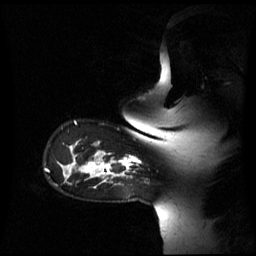
Breast MRI (dynamic contrast-enhanced), one sagittal slice; slice 49 of 60 in the series (ordered by position); dynamic contrast-enhanced series, image 2 of 3 at this slice position (ordered by acquisition); 1.5 T; TE 4.2 ms, TR 8.4 ms; 2.6 mm slice thickness; 256 × 256 image matrix, field of view 270 × 270 mm. Patient: female, 39 years. From the clinical record (not read from this slice): setting: breast cancer imaged before/during neoadjuvant chemotherapy; receptor status: triple-negative.
Structures marked on this image (semi-automatic segmentation, software-assisted and operator-edited):
- analysis volume of interest (the breast-tissue region the enhancement analysis was run in; not a lesion): bounding box (x1, y1, x2, y2) in pixels: (105, 156, 140, 176)
- tumour enhancement mask (voxels above the 70 % enhancement threshold inside the analysis volume of interest): (105, 157, 140, 176)